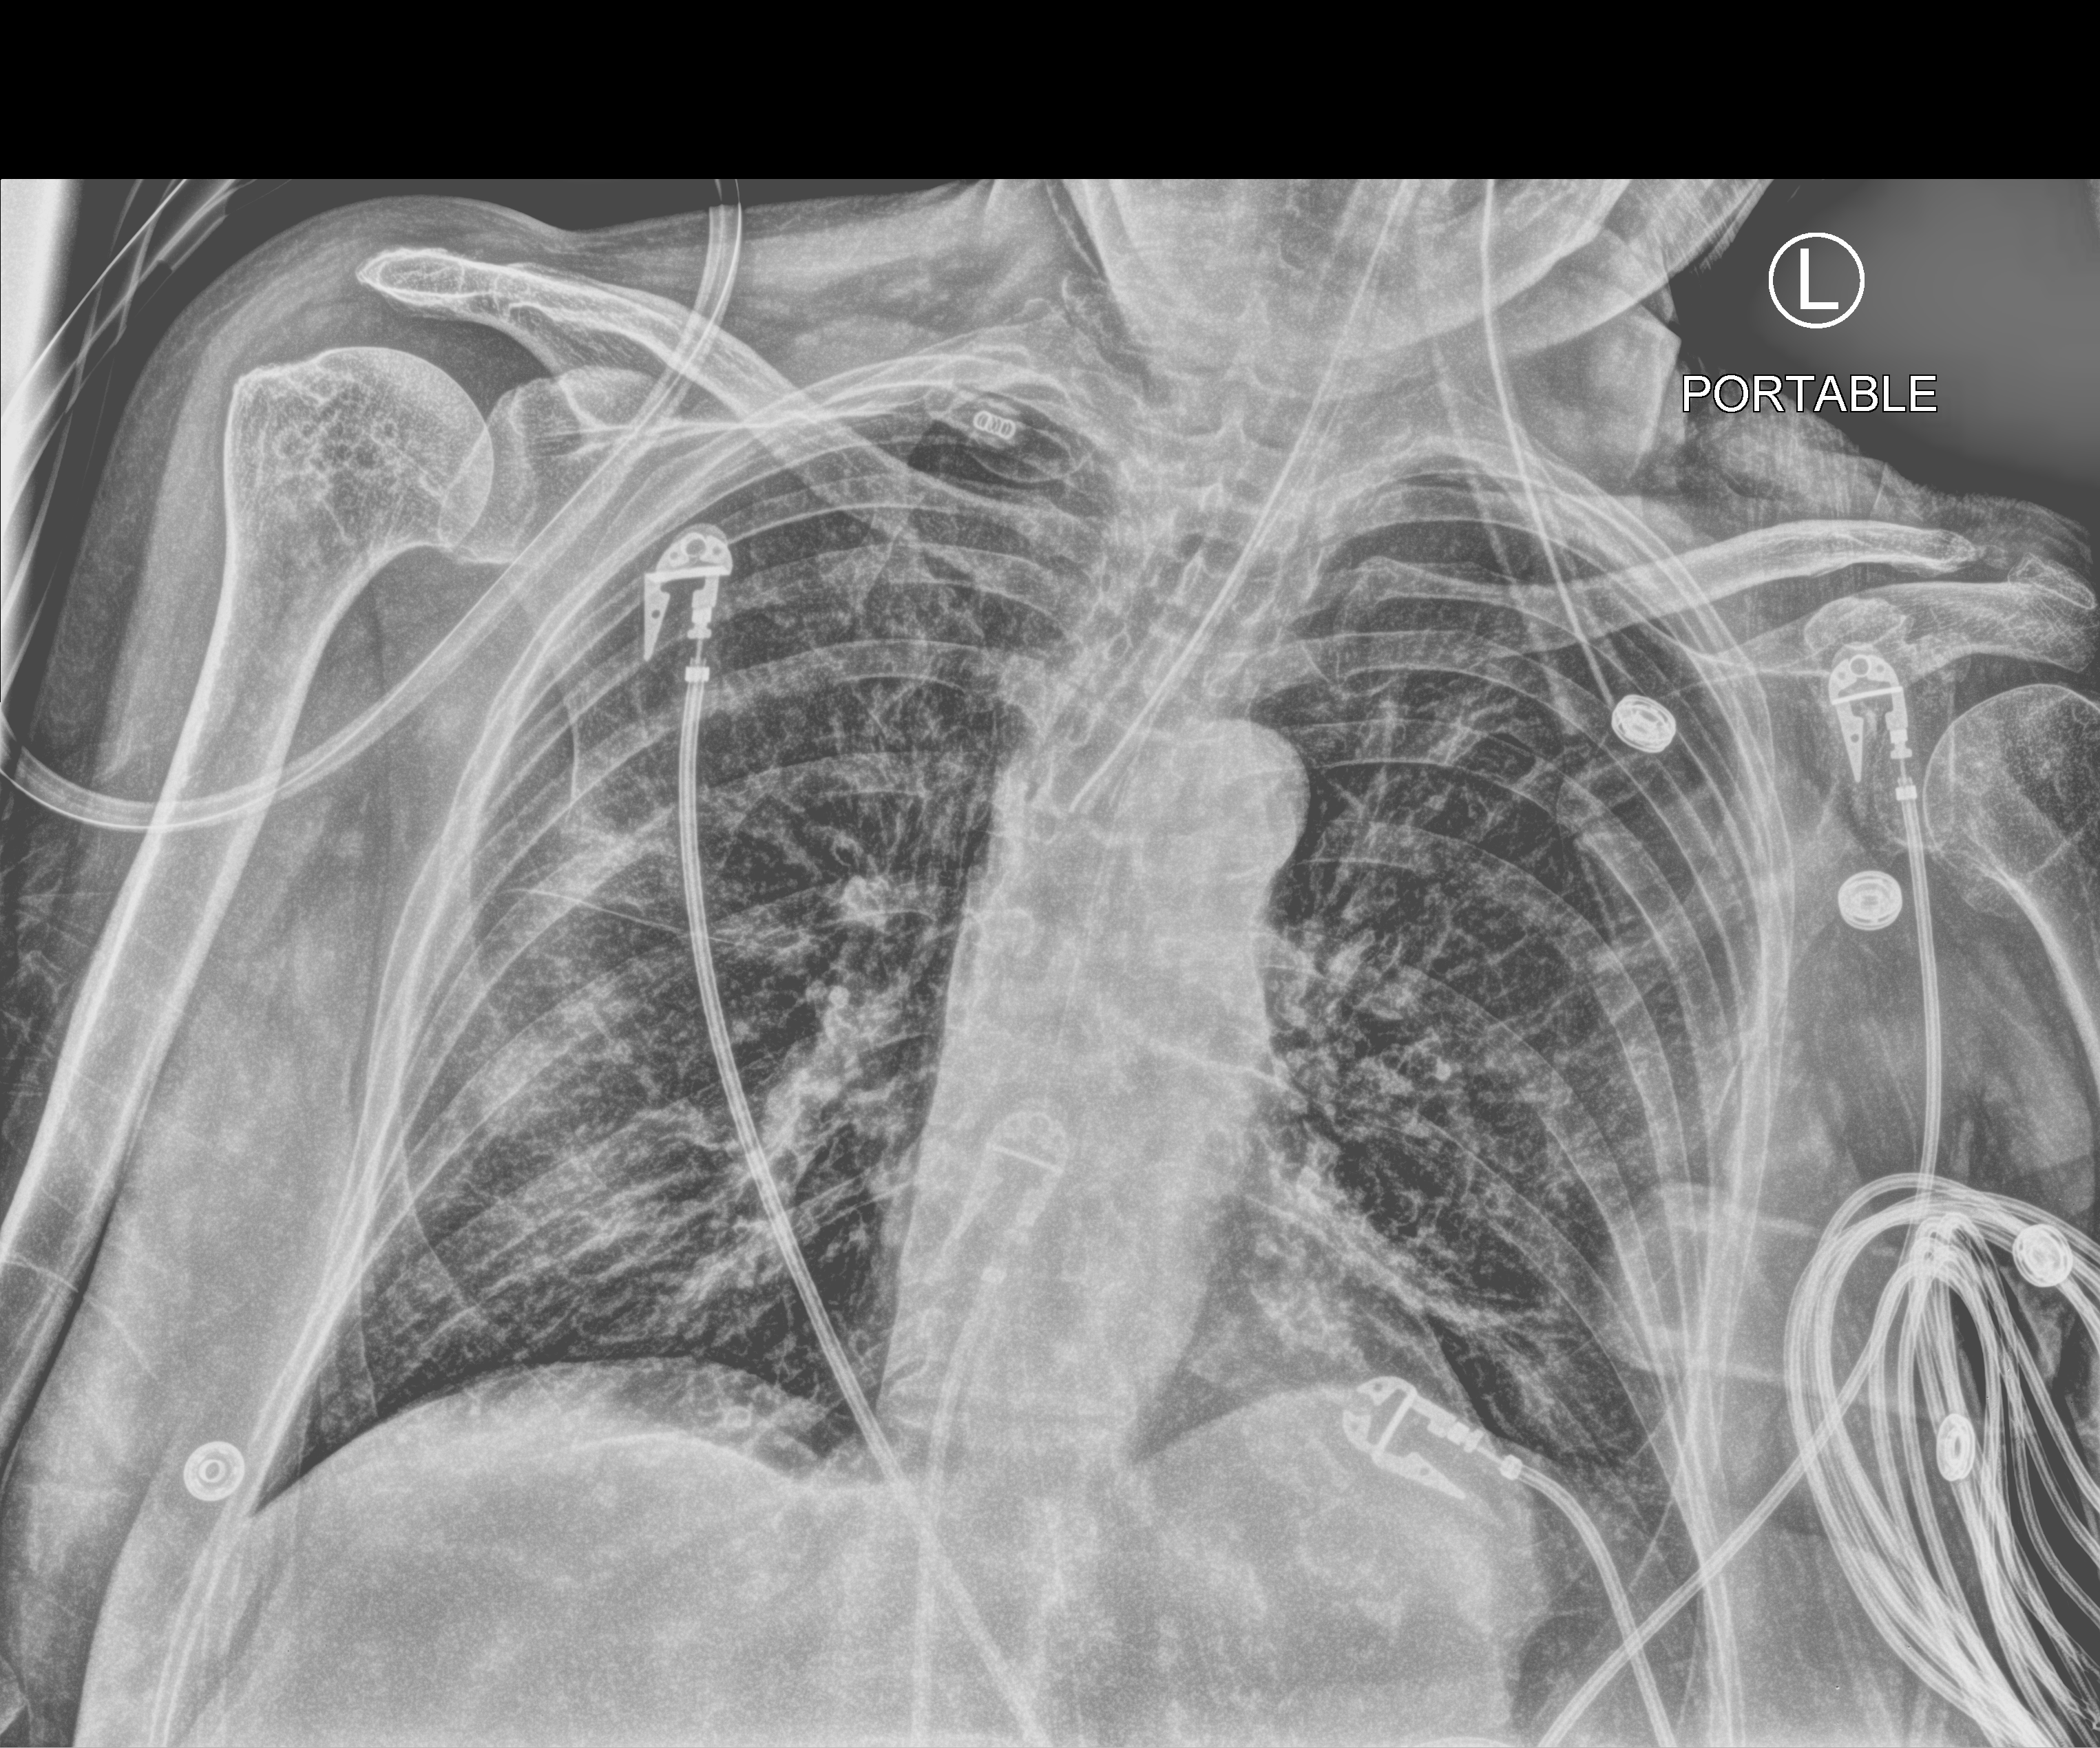
Portable chest radiograph, anteroposterior (AP) projection. Patient hospitalised with COVID-19; female, aged 75–90 years.
Admission-level facts for this patient (not findings on this image; timing relative to this image not recorded):
- chronic kidney disease (admission record): yes
- mechanically ventilated during this hospital stay: yes
- diabetes (admission record): no